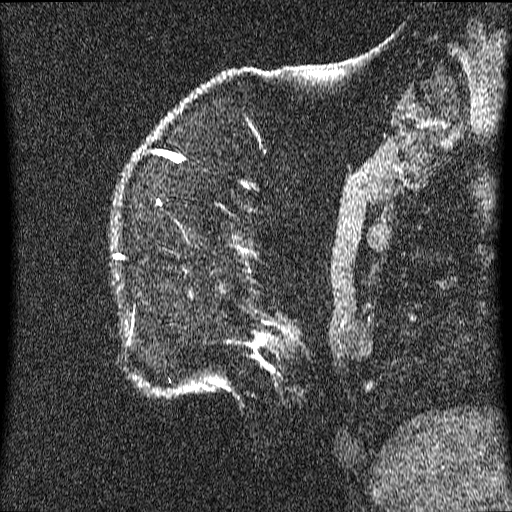
Breast MRI (dynamic contrast-enhanced), one sagittal slice. Position 9 of 64 along the scan axis. Dynamic contrast-enhanced series, image 2 of 3 at this slice position (ordered by acquisition). 1.5 T. TE 4.2 ms, TR 9.1 ms. 2.2 mm slice thickness. 512 × 512 image matrix, field of view 180 × 180 mm. Female patient, age 52 years.
Structures marked on this image (semi-automatic segmentation, software-assisted and operator-edited):
- analysis volume of interest (the breast-tissue region the enhancement analysis was run in; not a lesion): bounding box (x1, y1, x2, y2) in pixels: (116, 222, 348, 396)
- tumour enhancement mask (voxels above the 70 % enhancement threshold inside the analysis volume of interest): (117, 257, 262, 362)